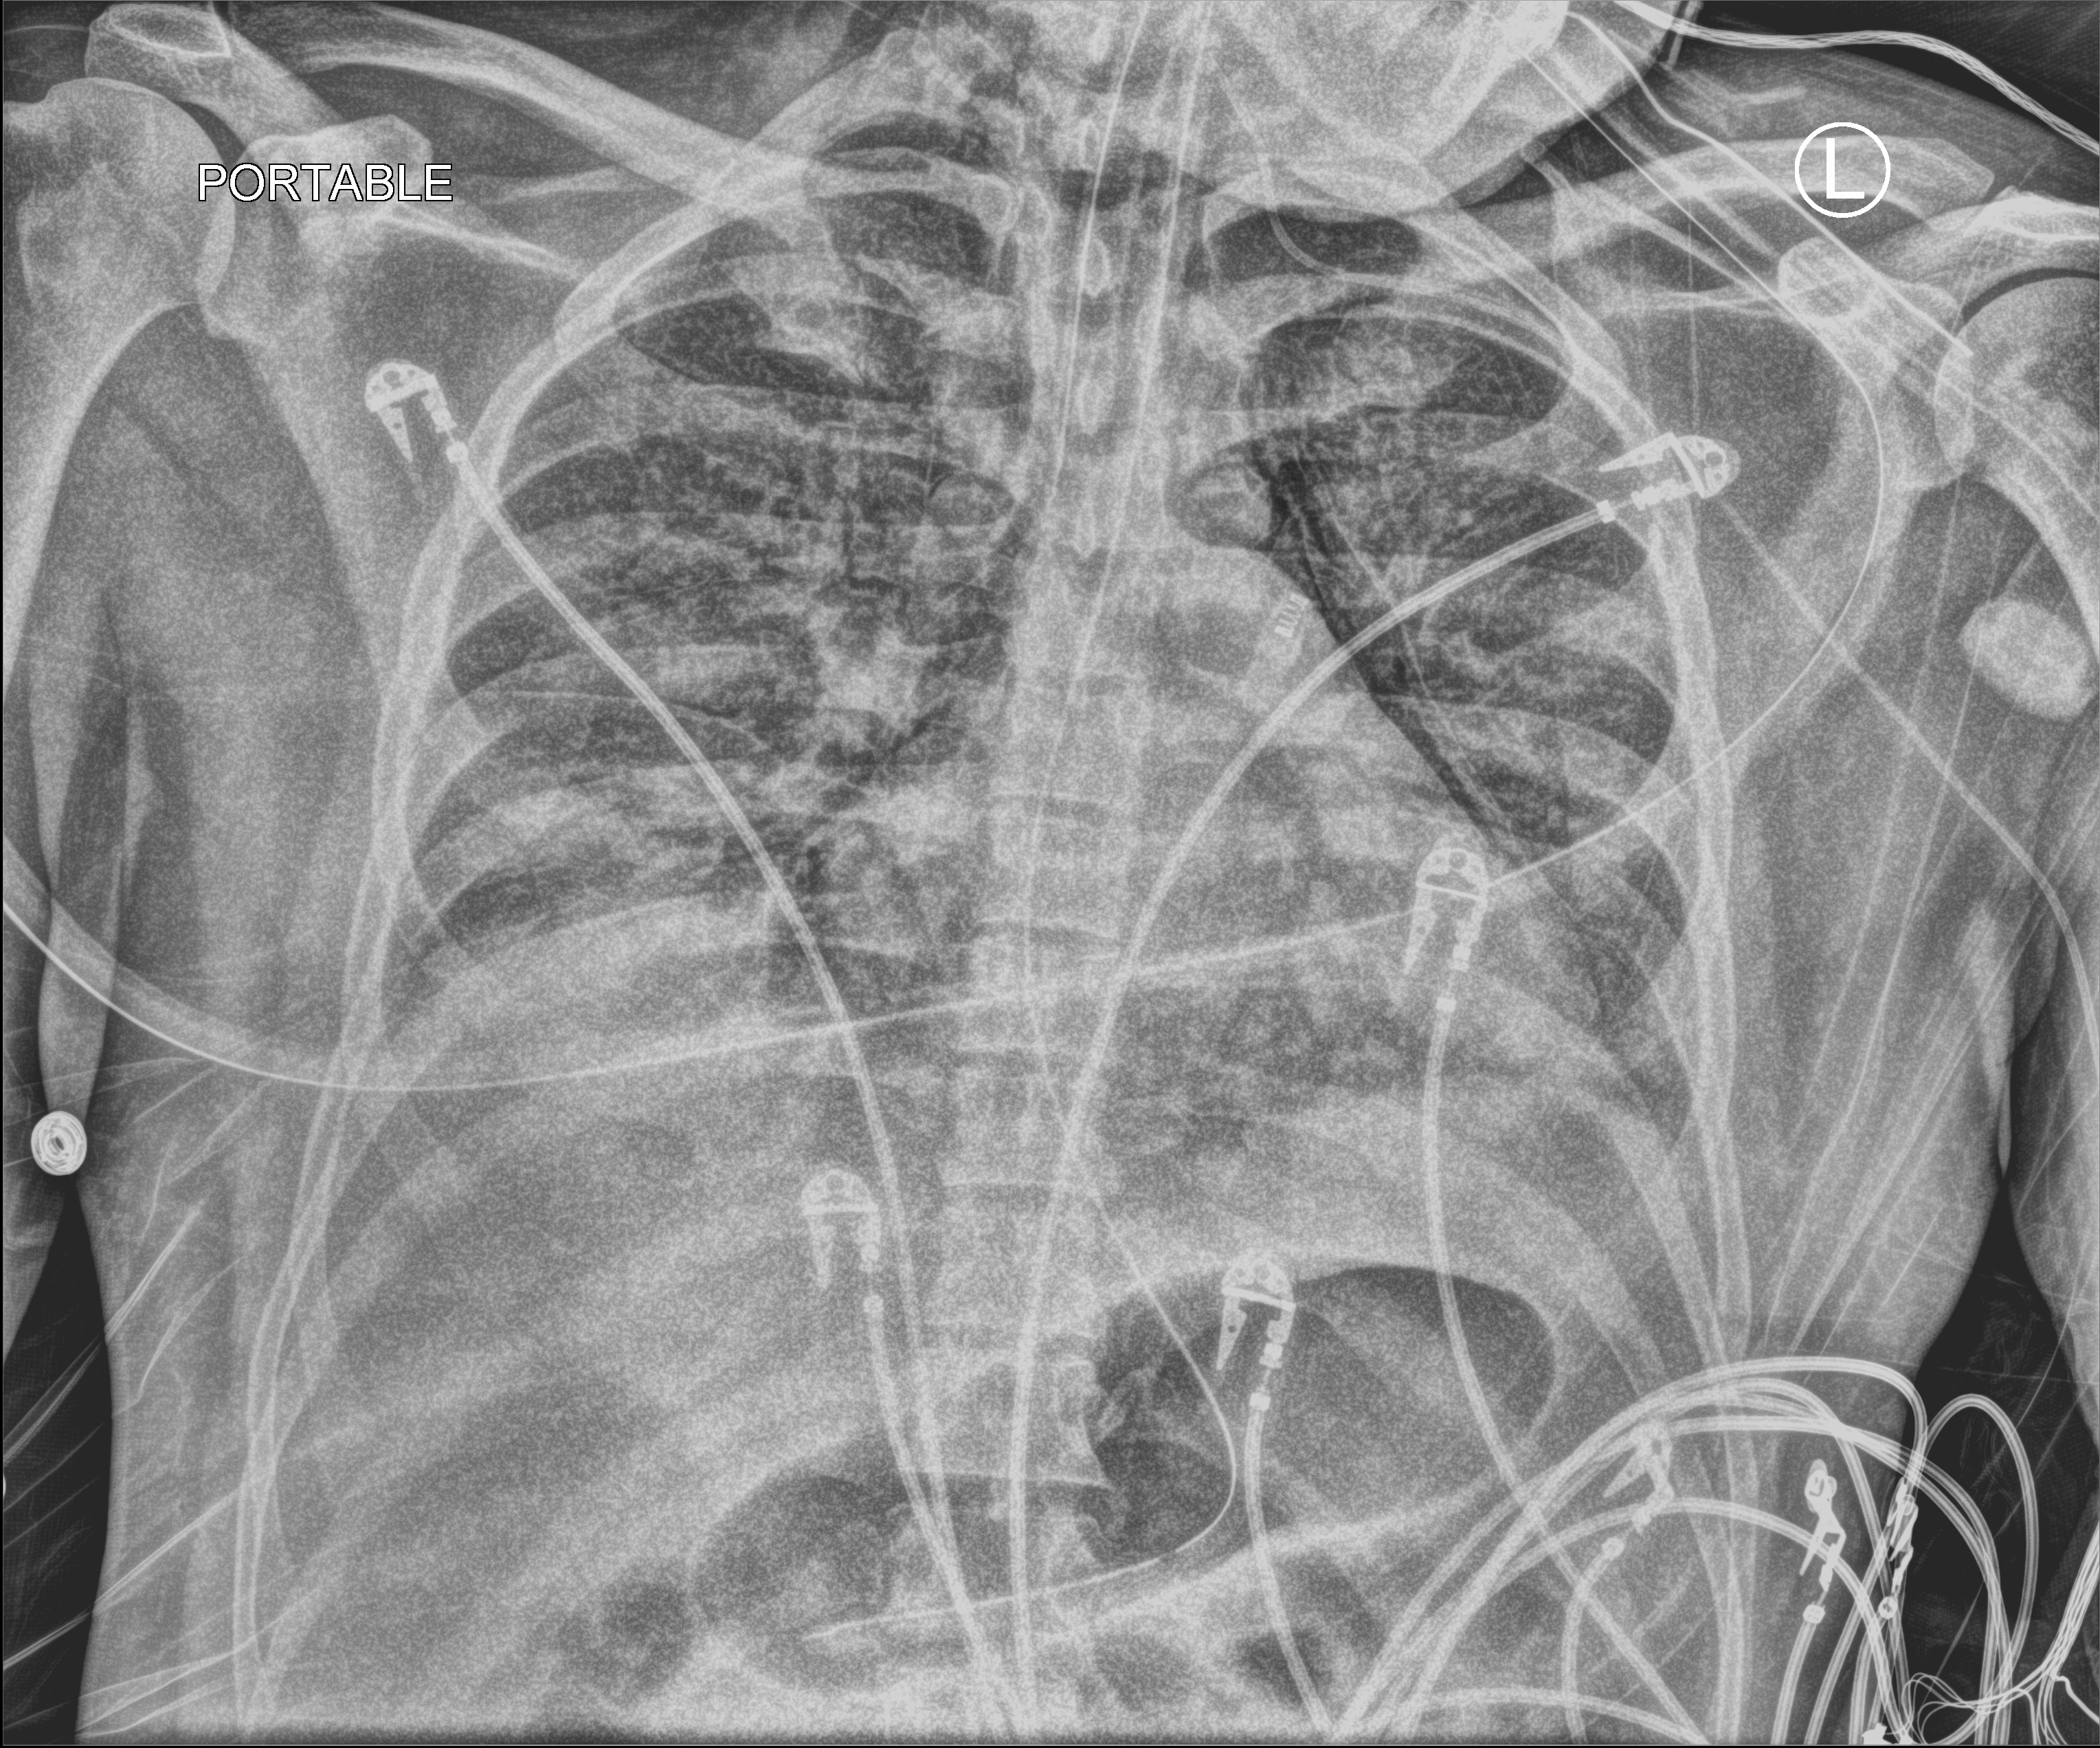
Portable chest radiograph; anteroposterior (AP) projection. Patient hospitalised with COVID-19; male, aged 18–59 years.
From the hospital-stay record, not from the radiograph (when in the stay this image was taken is not recorded): hypertension (admission record): no.